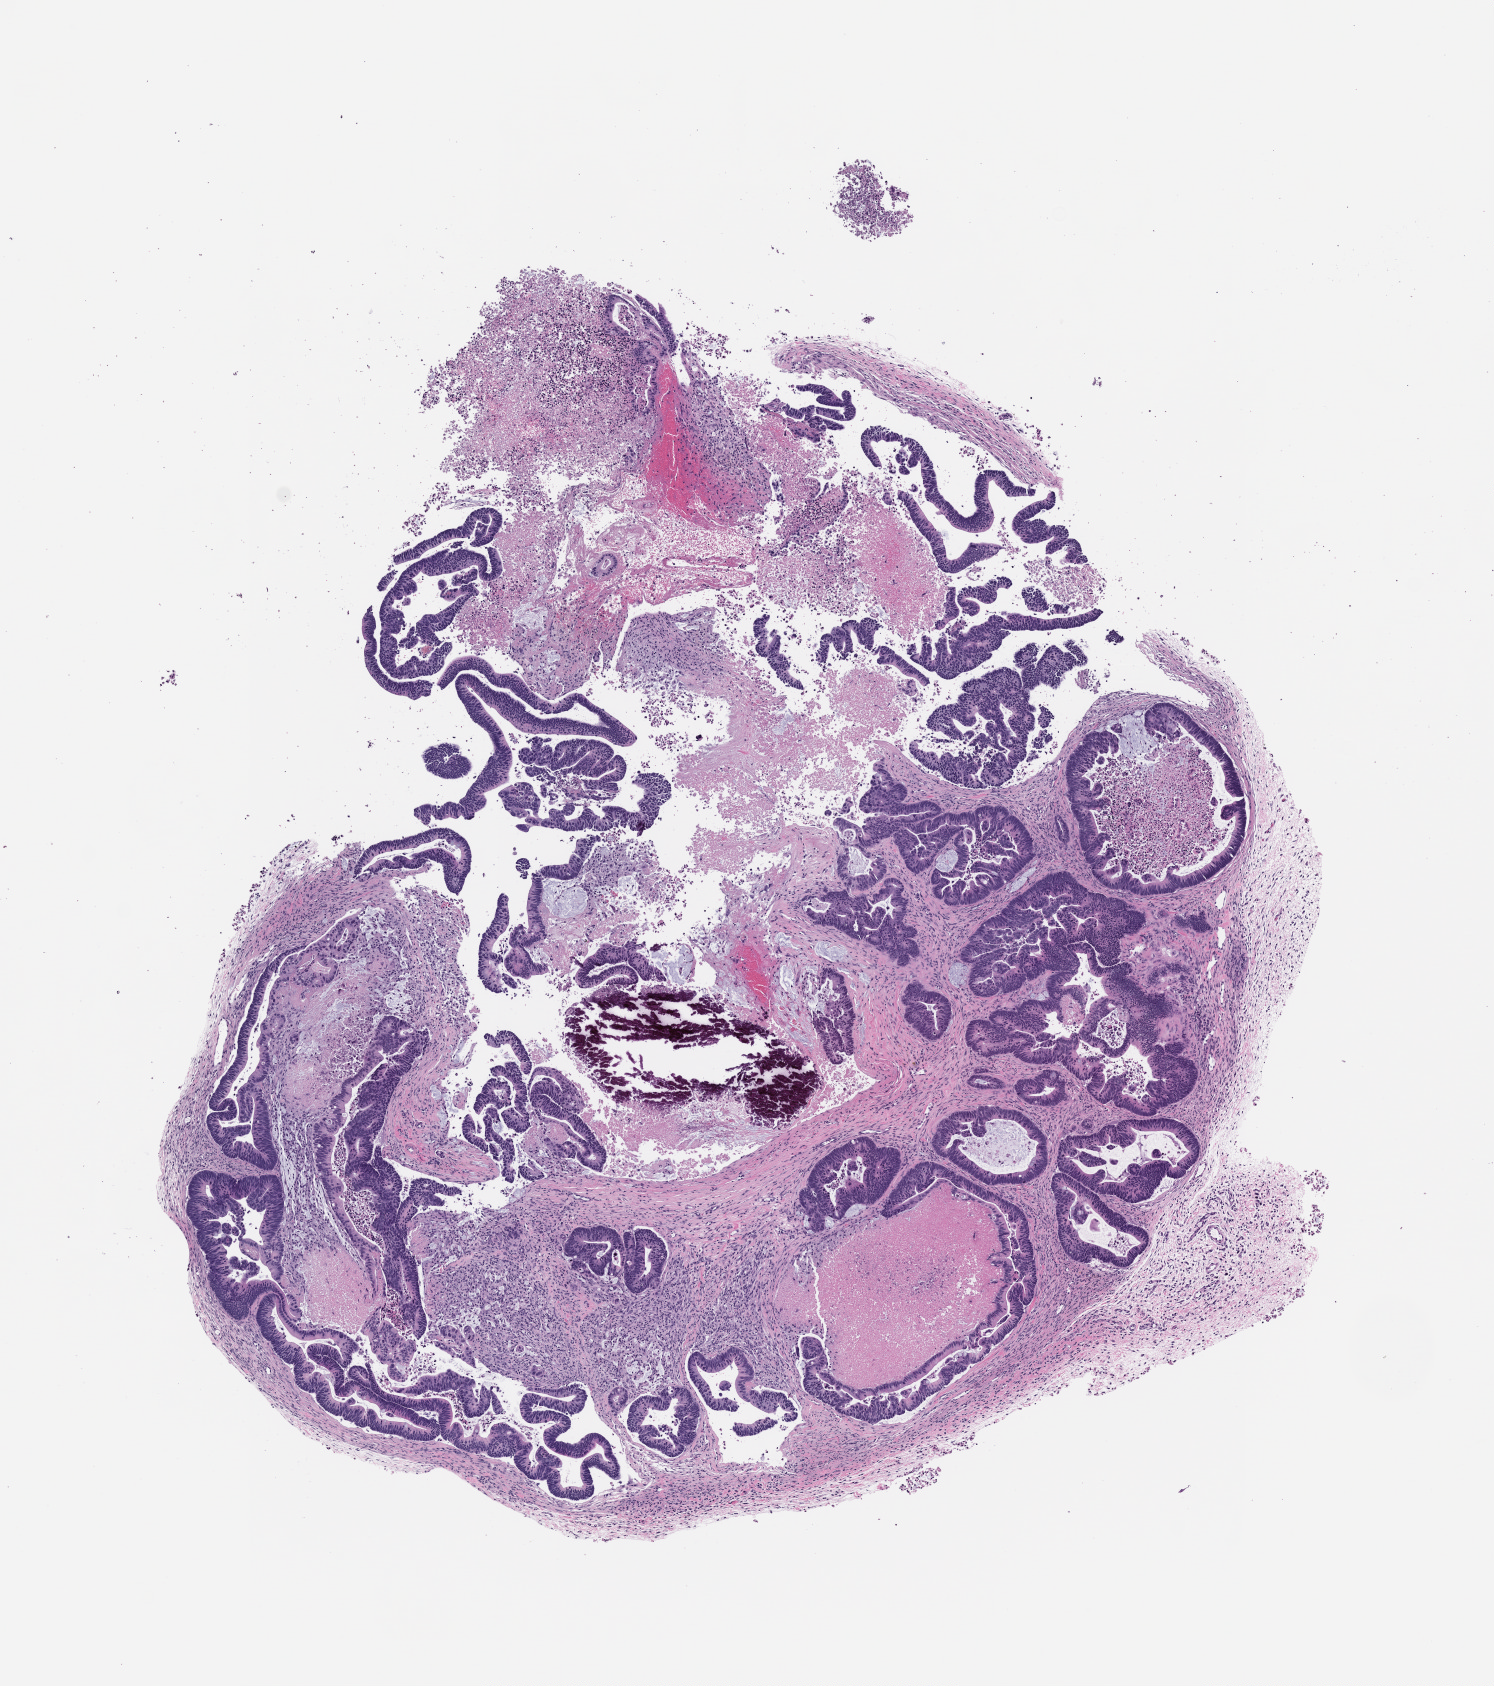
Haematoxylin and eosin whole-slide image of a patient-derived xenograft (PDX) tumor grown in a mouse, passage 3 — shown as a low-resolution overview of the whole scanned area (about 6.0 x 6.8 mm); FFPE section; originating tumor site category: colon.
Originating patient diagnosis: Colon Adenocarcinoma.